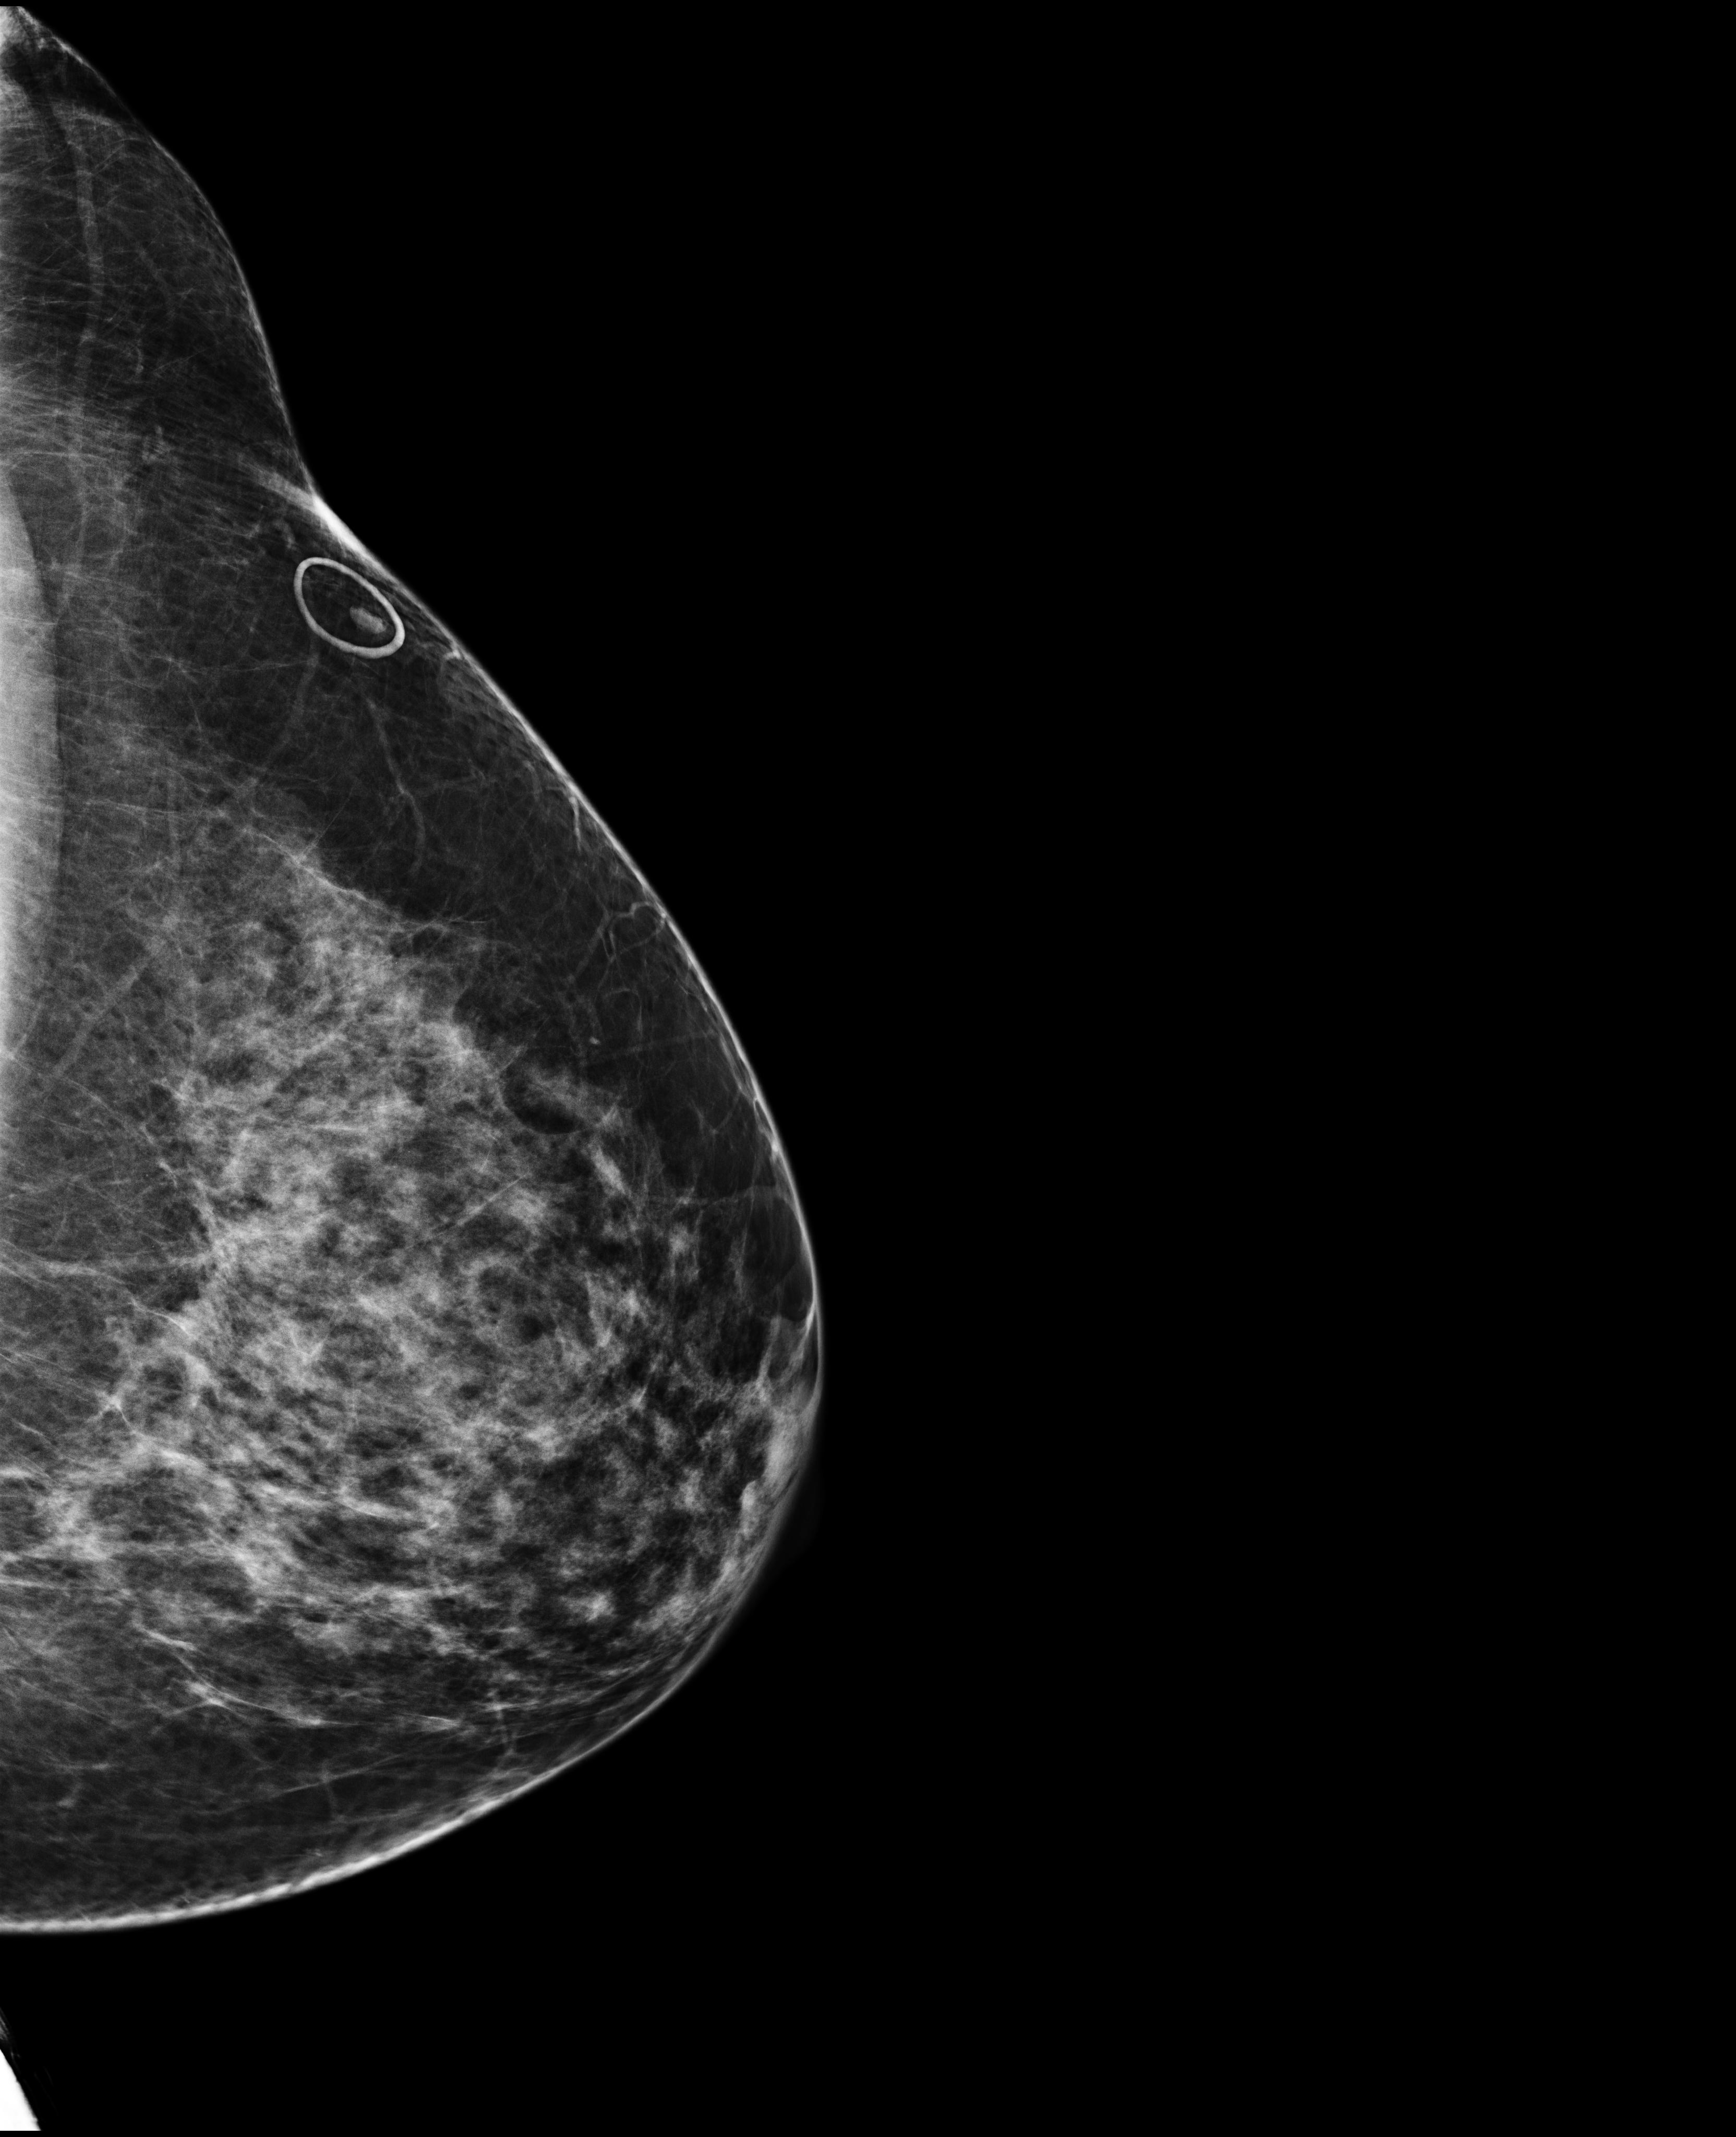
Annual screening mammography examination, compressed breast thickness 82 mm, system: Selenia Dimensions. Female patient, age 53 years.
Image type: full-field digital mammogram. Breast: left. Projection: exaggerated CC view (lateral).